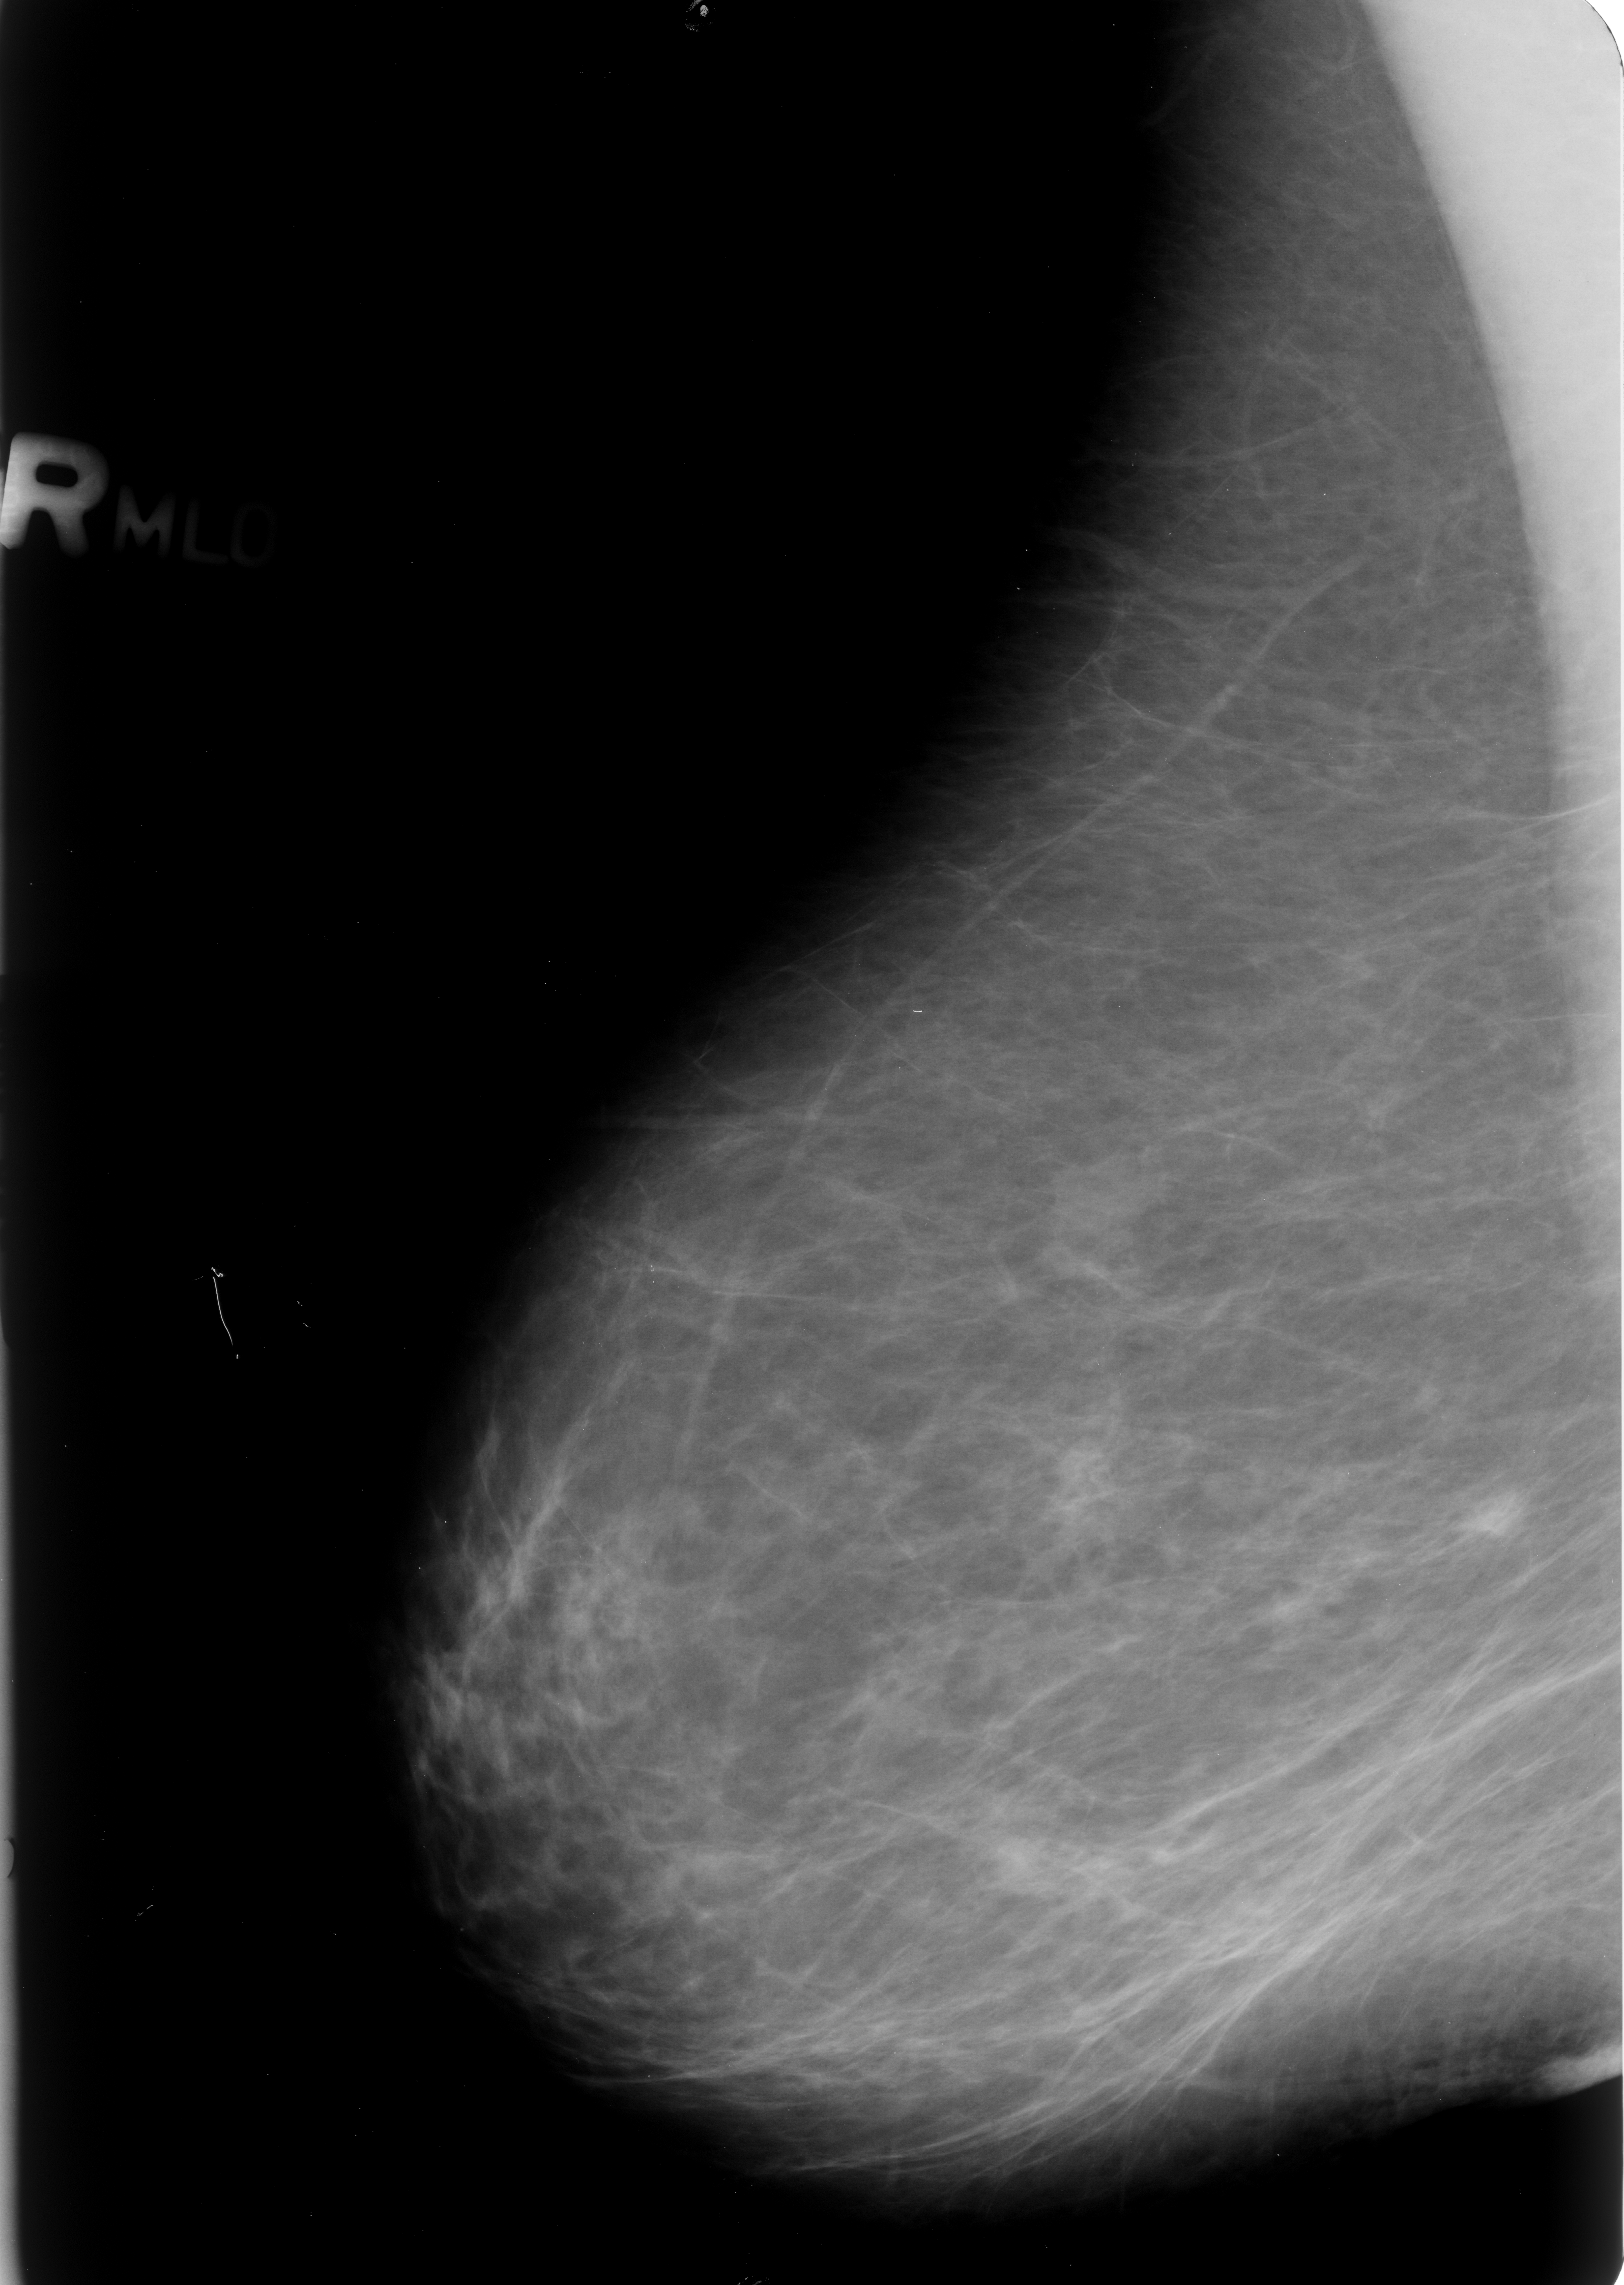
Scanned film-screen mammogram; right breast; mediolateral oblique (MLO) view; BI-RADS breast density category 1 (scale 1–4).
Abnormality record for this image: mass, shape oval, margins ill defined; BI-RADS assessment category 4; pathology (as recorded): malignant.